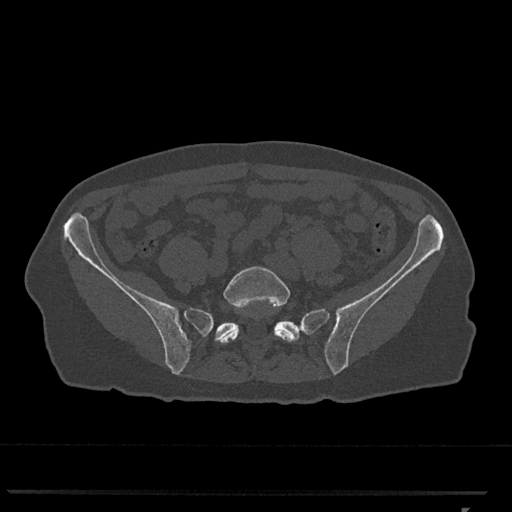
CT including the spine, one axial slice. Reconstruction kernel Br40s/3. 120 kVp. Bone window (W 1800 / L 400 HU). 0.5 mm slice thickness. 512 × 512 image matrix, field of view 380 × 380 mm. Patient: female, 62 years. Case-level facts recorded for this patient, not image findings: primary cancer: renal.
Structures marked on this image (semi-automatic segmentation, software-assisted and operator-edited):
- L5 vertebra: box from (x=217, y=266) to (x=297, y=343) px